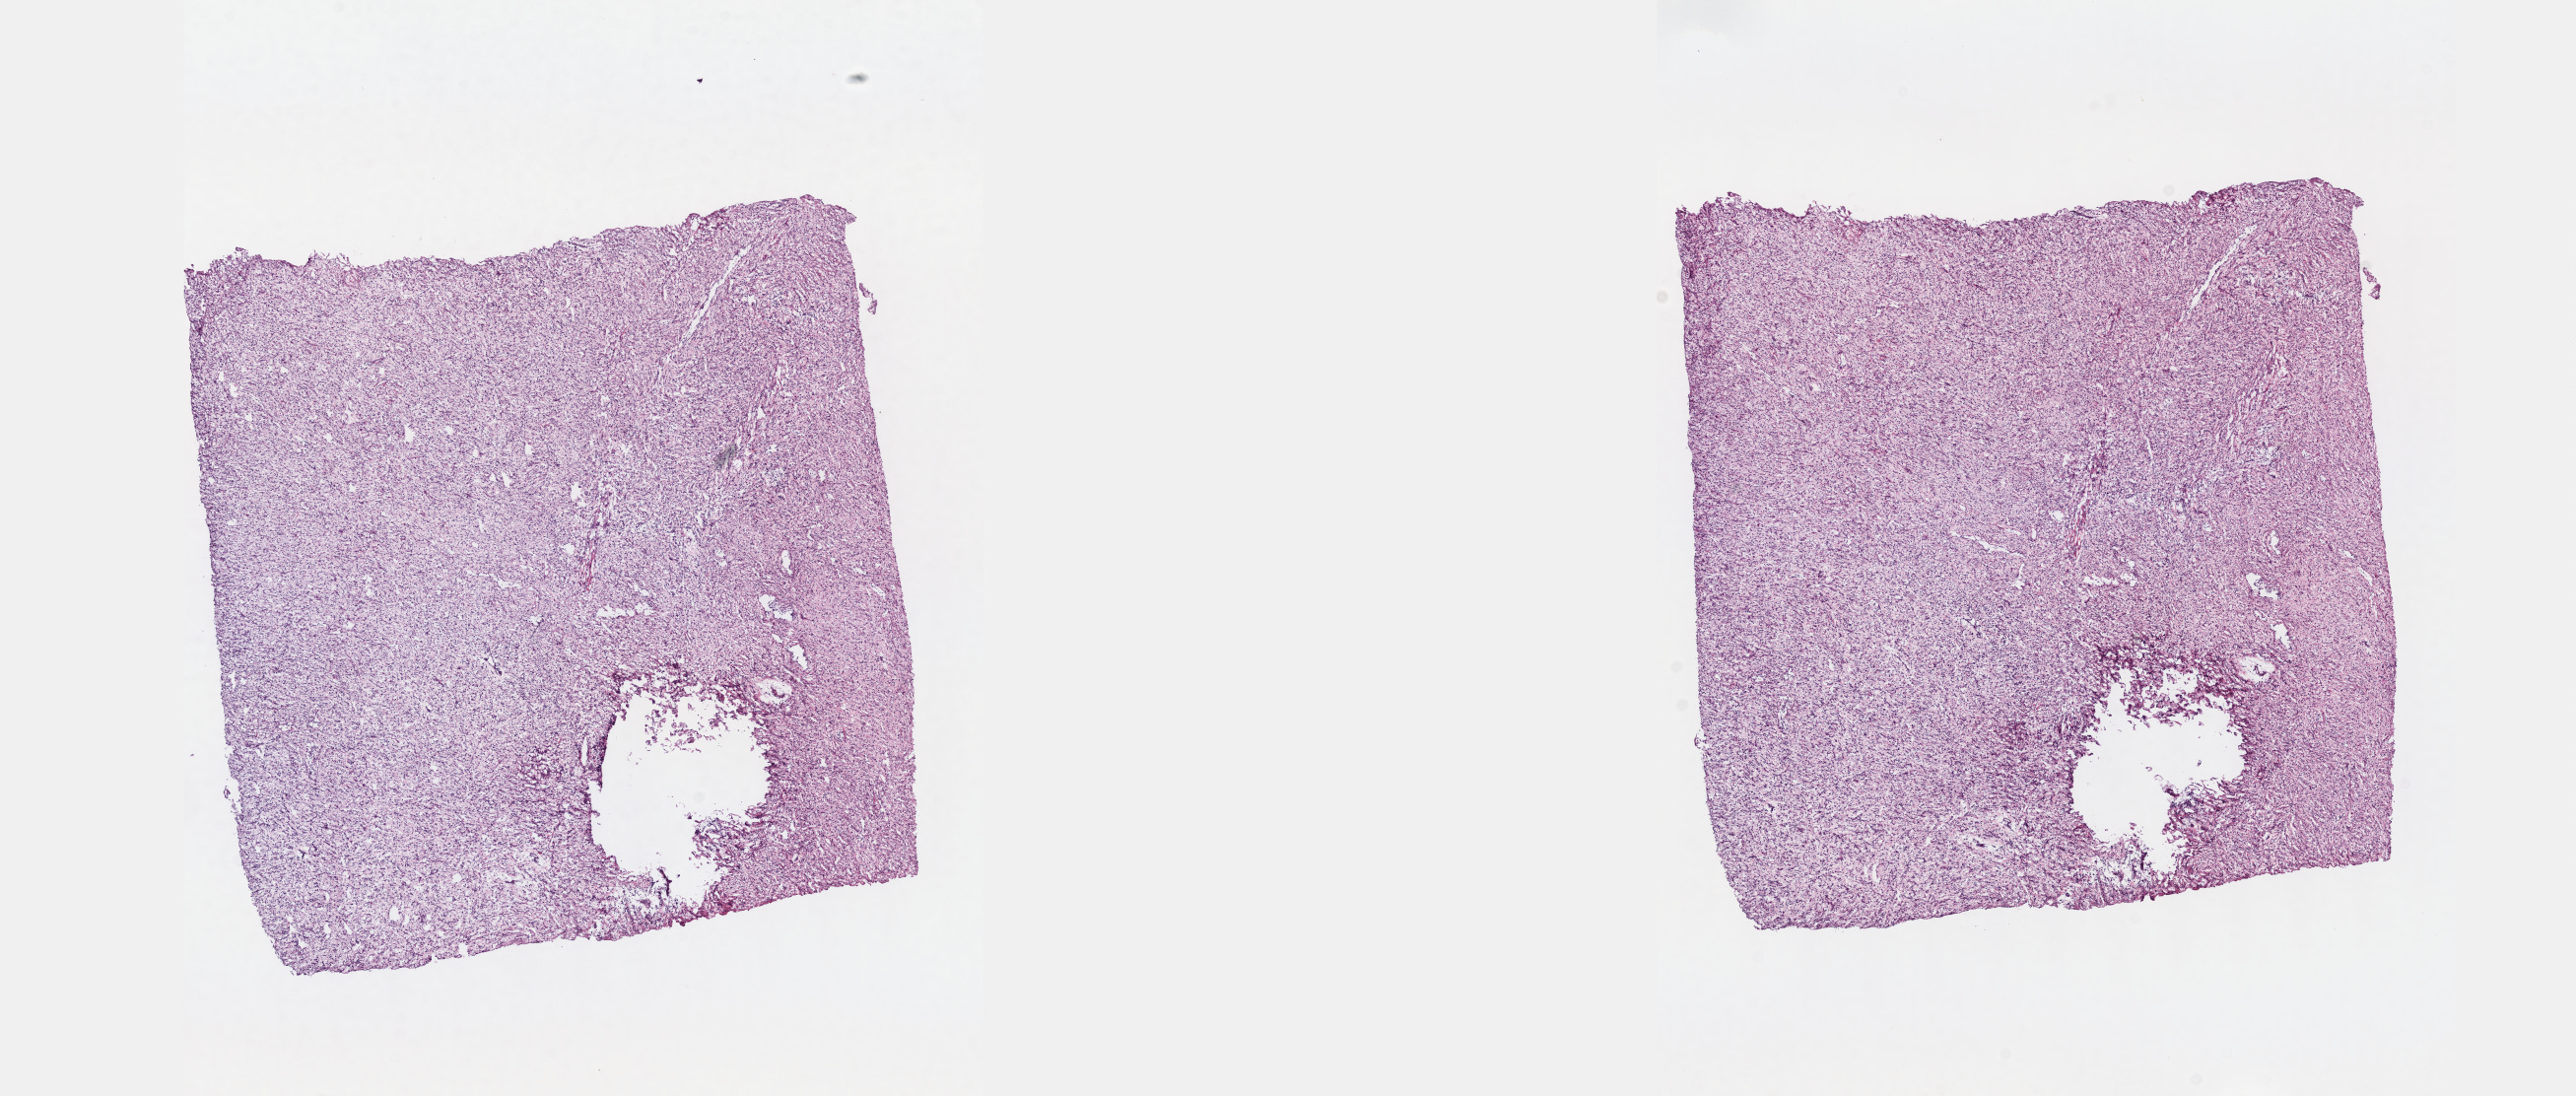
Digitized H&E-stained tissue section (whole slide), whole scanned area (about 21.1 x 9.0 mm, acquisition: 40x scan) shown as a low-resolution overview, frozen section, sample: primary tumour, connective, subcutaneous and other soft tissues. Male patient; age at initial diagnosis 37 years. Composition of this section per pathologist review: tumour cells 90%, tumour nuclei 95%, normal cells 0%, stromal cells 10%, necrosis 0%. Inflammatory infiltration, as recorded: lymphocyte infiltration 0%, monocyte infiltration 0%, neutrophil infiltration 0%.
• histologic diagnosis: Dedifferentiated liposarcoma